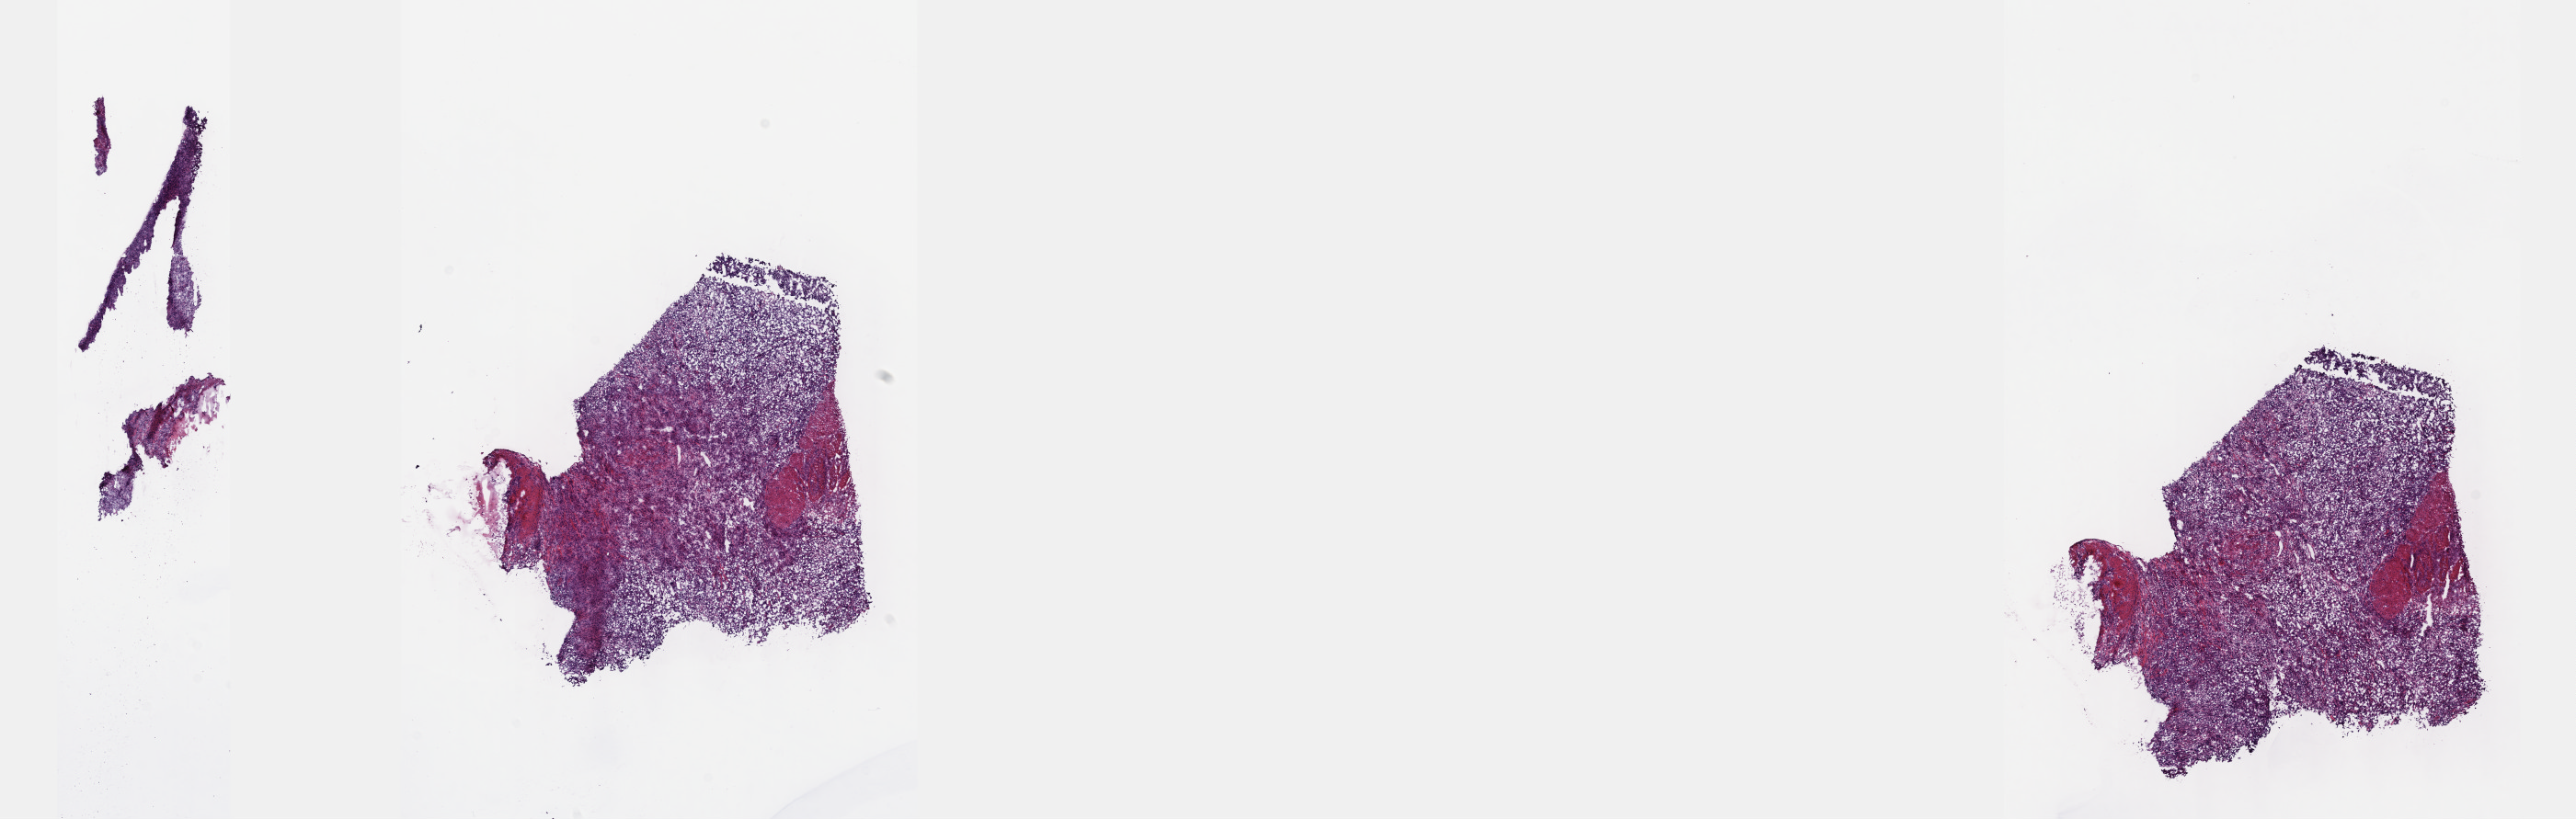
Digitized H&E-stained tissue section (whole slide) — low-resolution overview of the scanned area, about 22.6 x 7.2 mm. Frozen section. Bladder, primary tumour sample. Patient: female, age at initial diagnosis 61 years. Histologic grade: high grade. Slide review estimates, as recorded: tumour cells 70%, tumour nuclei 90%, normal cells 0%, stromal cells 20%, necrosis 10%. Infiltration values recorded for this section: lymphocyte infiltration 0%, monocyte infiltration 0%, neutrophil infiltration 0%.
- pathologic diagnosis: Transitional cell carcinoma
- TNM: T3a N2 MX
- lymph nodes positive (case pathology): 2 of 11 examined
- AJCC pathologic stage: IV